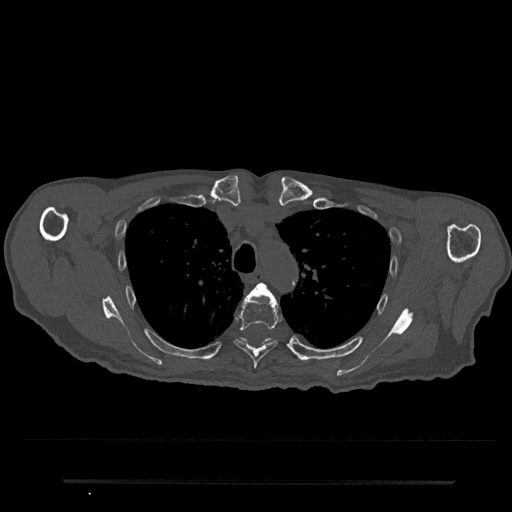
CT including the spine, one axial slice; reconstruction kernel Br40s/3; 120 kVp; bone window (W 1800 / L 400 HU); 0.5 mm slice thickness; 512 × 512 image matrix, field of view 427 × 427 mm. Male patient, age 74 years. Case-level facts recorded for this patient, not image findings: primary cancer: prostate.
Annotated regions visible in this slice (semi-automatically segmented with operator editing):
- T4 vertebra: bounding box <248,283,273,298> (left, top, right, bottom; pixels)
- T5 vertebra: <234,294,279,369>
- T6 vertebra: <239,338,272,344>